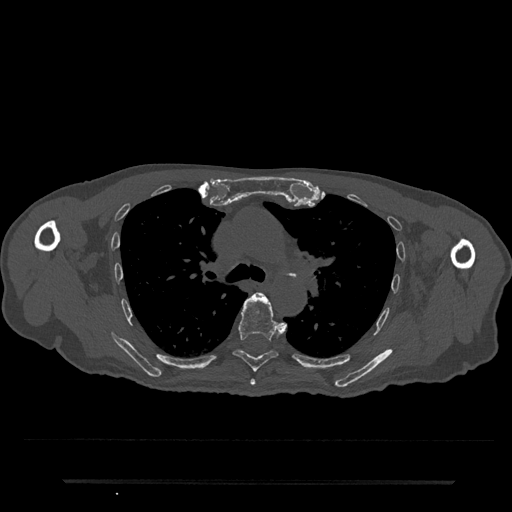
CT including the spine, one axial slice. Slice 532 of 797 in the series (ordered by position). Bone window (W 1800 / L 400 HU). 0.5 mm slice thickness. 512 × 512 image matrix, field of view 427 × 427 mm. Male patient, age 74 years. Case-level facts recorded for this patient, not image findings: primary cancer: prostate.
Annotated regions visible in this slice (semi-automatic segmentation, software-assisted and operator-edited):
- T5 vertebra: bounding box (x1, y1, x2, y2) in pixels: (250, 379, 256, 386)
- T6 vertebra: (233, 292, 282, 372)